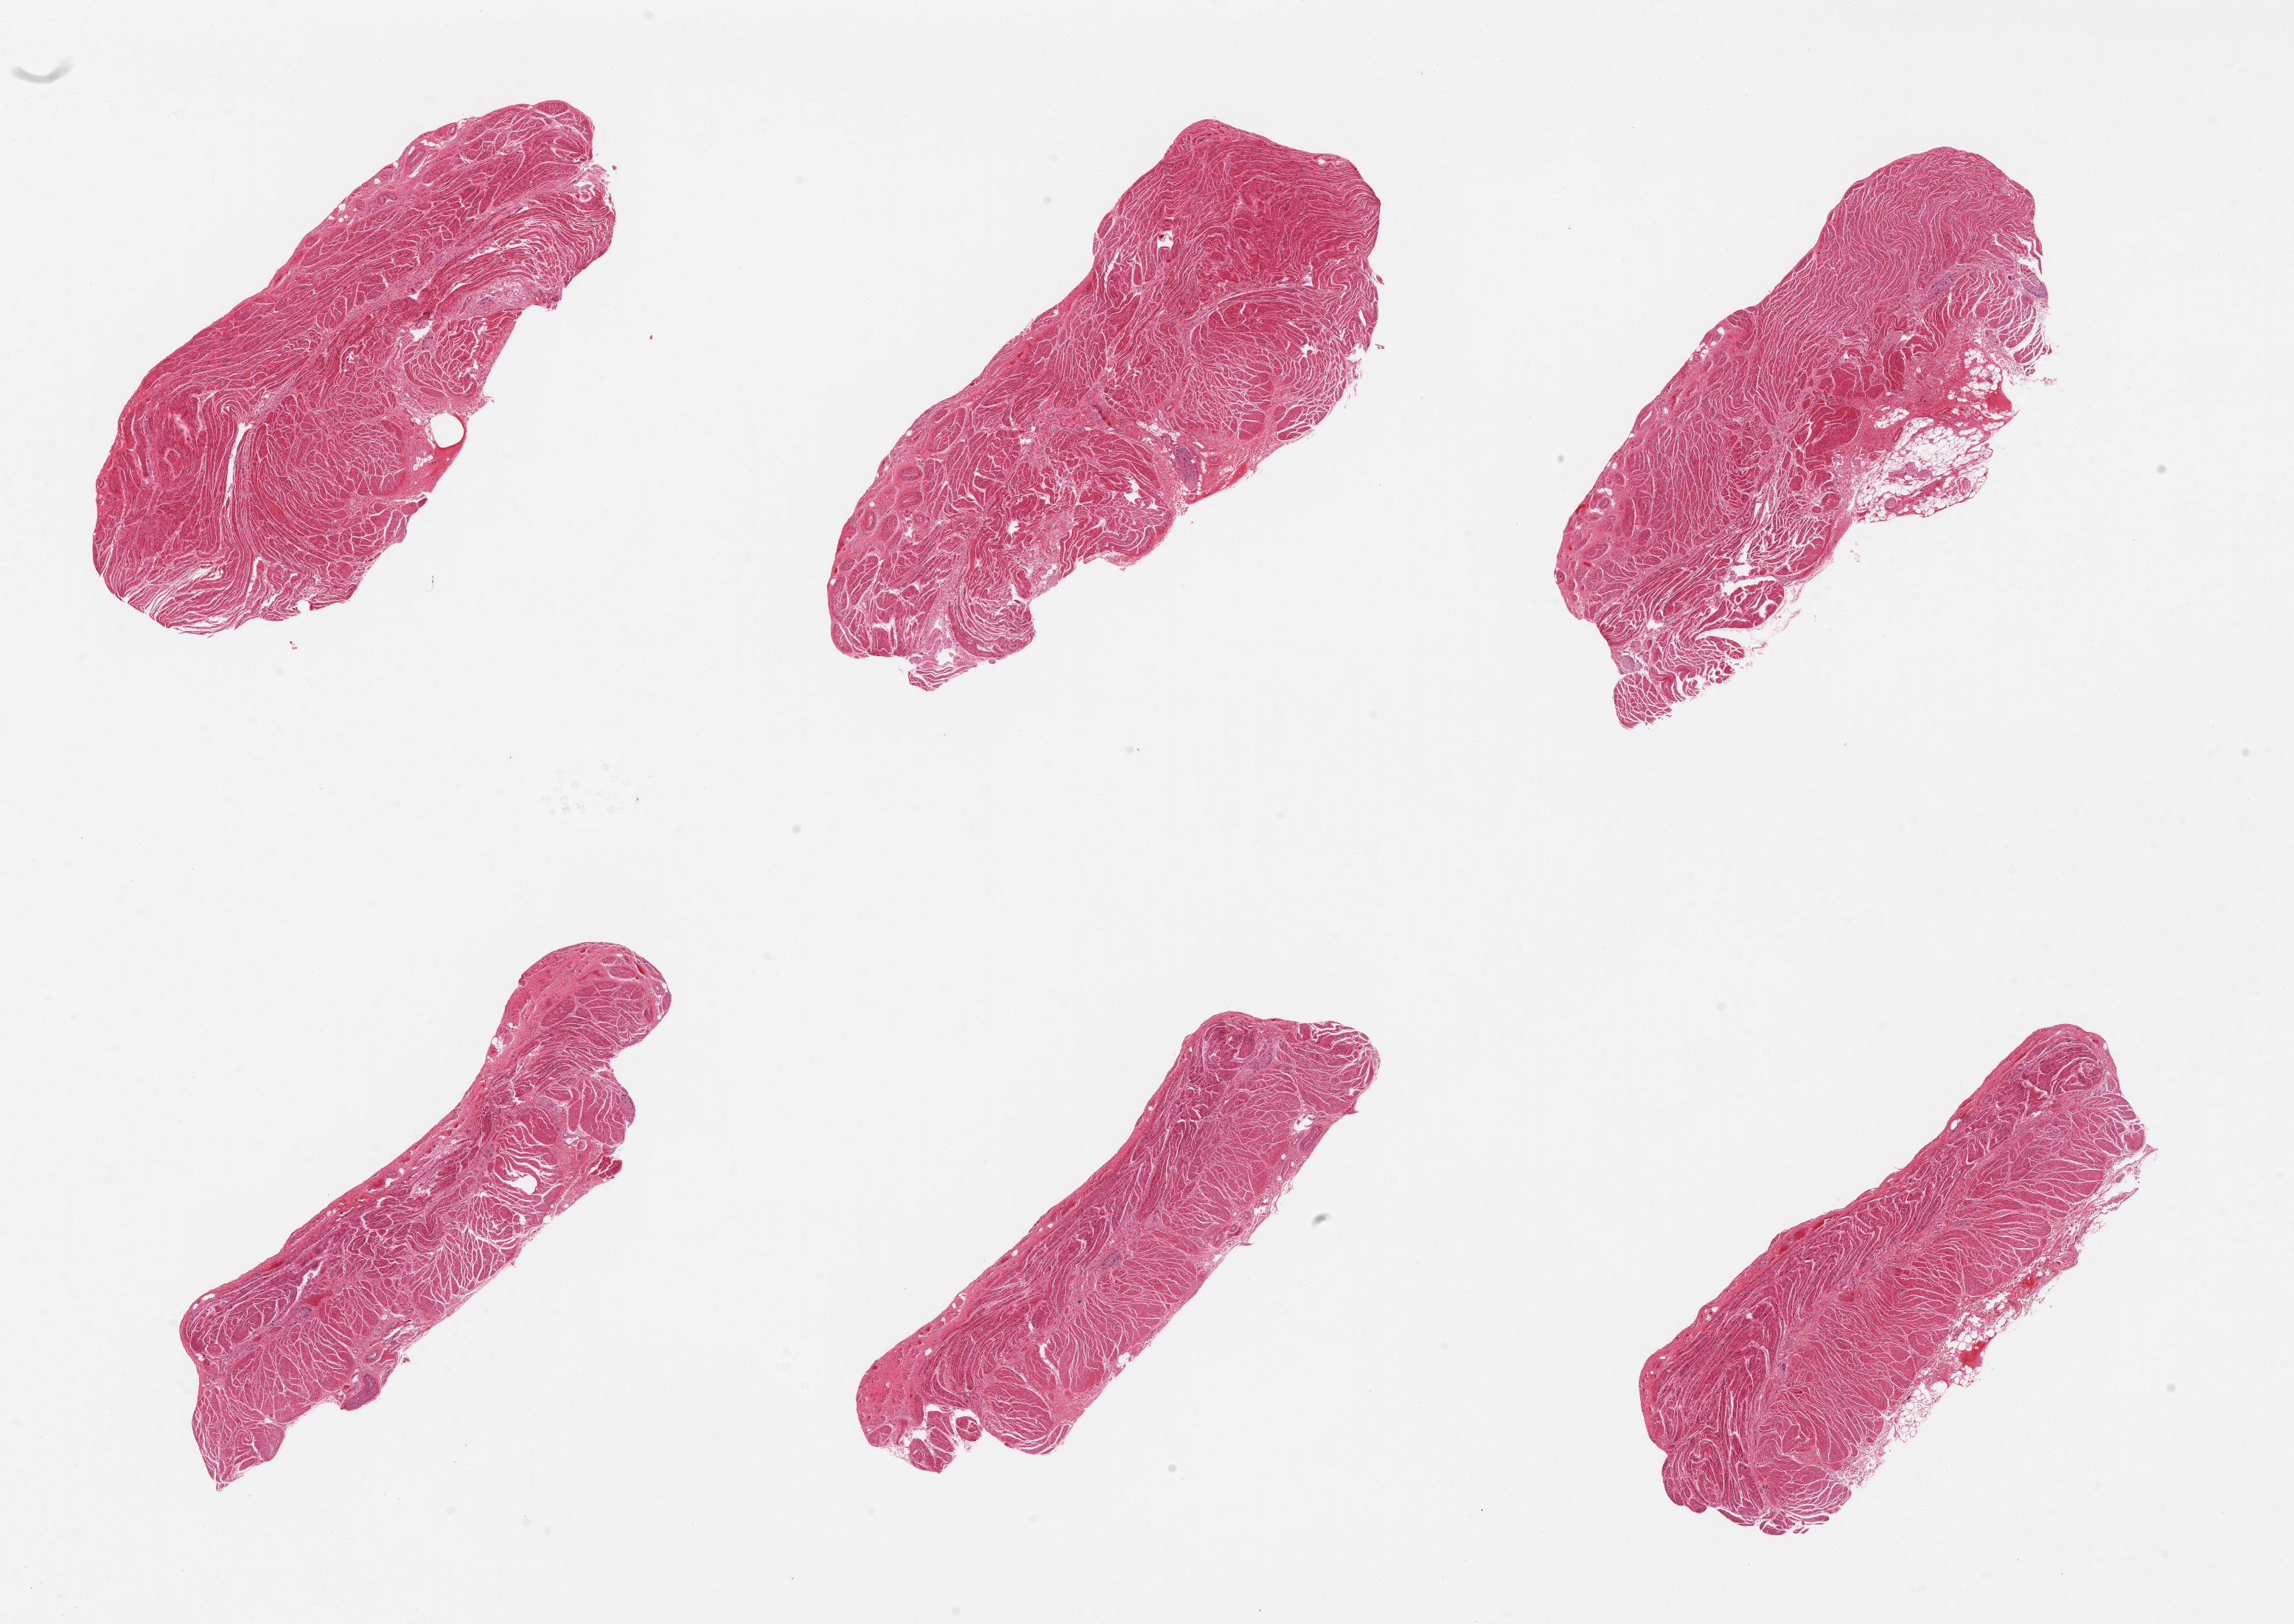
H&E whole-slide image — whole scanned area (about 24.6 x 17.4 mm, acquisition: 20x scan) shown as a low-resolution overview. PAXgene-fixed paraffin-embedded (PFPE) section. Target tissue: gastroesophageal junction. Tissue donor sample.
* review note (as recorded): 6 pieces, all muscularis, good specimens